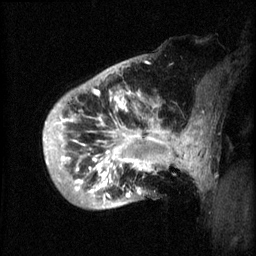
Breast MRI (dynamic contrast-enhanced), one sagittal slice; 3 images stored at this slice position (order not interpretable as contrast timing); 1.5 T; TE 4.2 ms, TR 8.2 ms; 2 mm slice thickness; 256 × 256 image matrix. Female patient, age 50 years.
Structures marked on this image (semi-automatically segmented with operator editing):
- analysis volume of interest (the breast-tissue region the enhancement analysis was run in; not a lesion): bounding box <44,72,173,211> (left, top, right, bottom; pixels)
- tumour enhancement mask (voxels above the 70 % enhancement threshold inside the analysis volume of interest): <44,90,173,201>